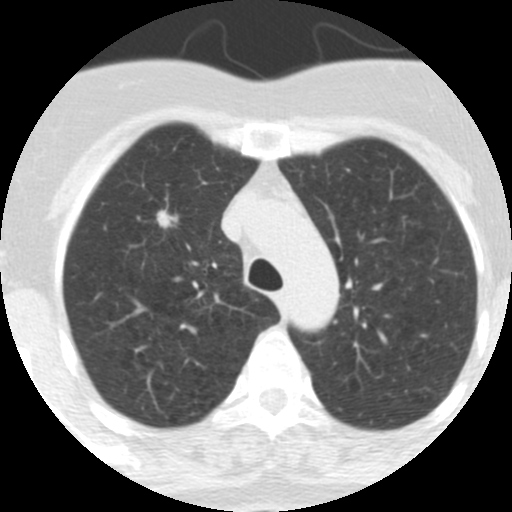
Low-dose screening chest CT, one axial slice. Position 239 of 313 along the scan axis. Lung window (W 1500 / L -600 HU). 2.5 mm slice thickness. 512 × 512 image matrix, field of view 253 × 253 mm.
Outlined on this slice (outlined manually by an expert reader):
- lesion 1 (tumor, upper lobe of right lung): bounding box [x1, y1, x2, y2] px = [157, 209, 178, 228]